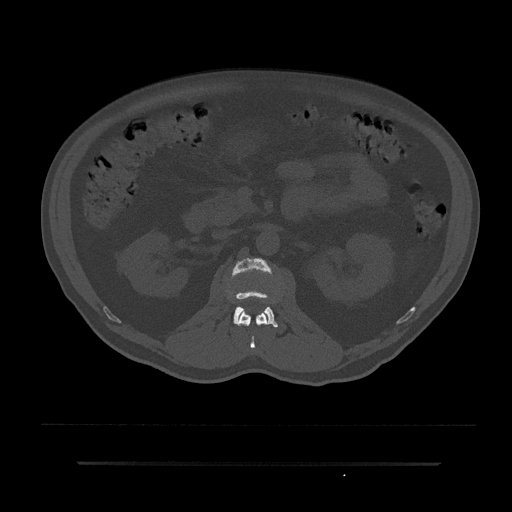
CT including the spine, one axial slice; slice 108 of 797 in the series (ordered by position); reconstruction kernel Br40s/3; 120 kVp; bone window (W 1800 / L 400 HU); 0.5 mm slice thickness; 512 × 512 image matrix. Patient: male, 59 years. From the clinical record (not read from this slice): primary cancer: bile ducts; vertebrae with lytic lesions (as recorded): T10.
Structures marked on this image (semi-automatic segmentation, software-assisted and operator-edited):
- L1 vertebra: bounding box [x1, y1, x2, y2] px = [238, 309, 267, 349]
- L2 vertebra: [233, 258, 278, 327]